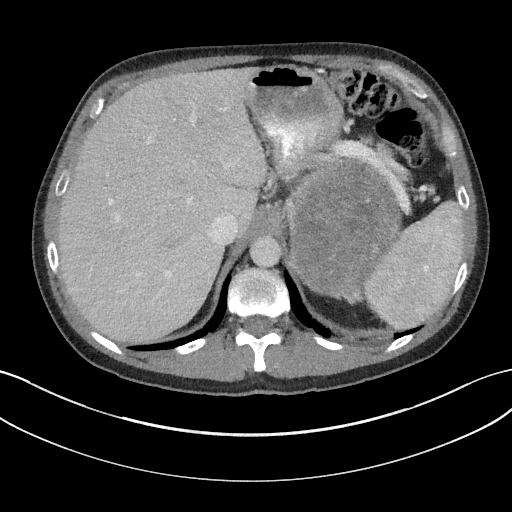
Contrast-enhanced abdominal CT, one axial slice; slice 125 of 147 in the series (ordered by position); reconstruction kernel I31f/3; 100 kVp; intravenous contrast given; soft-tissue window (W 400 / L 40 HU); 3 mm slice thickness; 512 × 512 image matrix. Male patient, age 58 years. From the clinical record (not read from this slice): diagnosis: adrenocortical carcinoma; tumour side: left adrenal; tumour size at pathology: 22 cm.
Structures marked on this image (semi-automatic segmentation, software-assisted and operator-edited):
- mass: box from (x=290, y=166) to (x=395, y=294) px